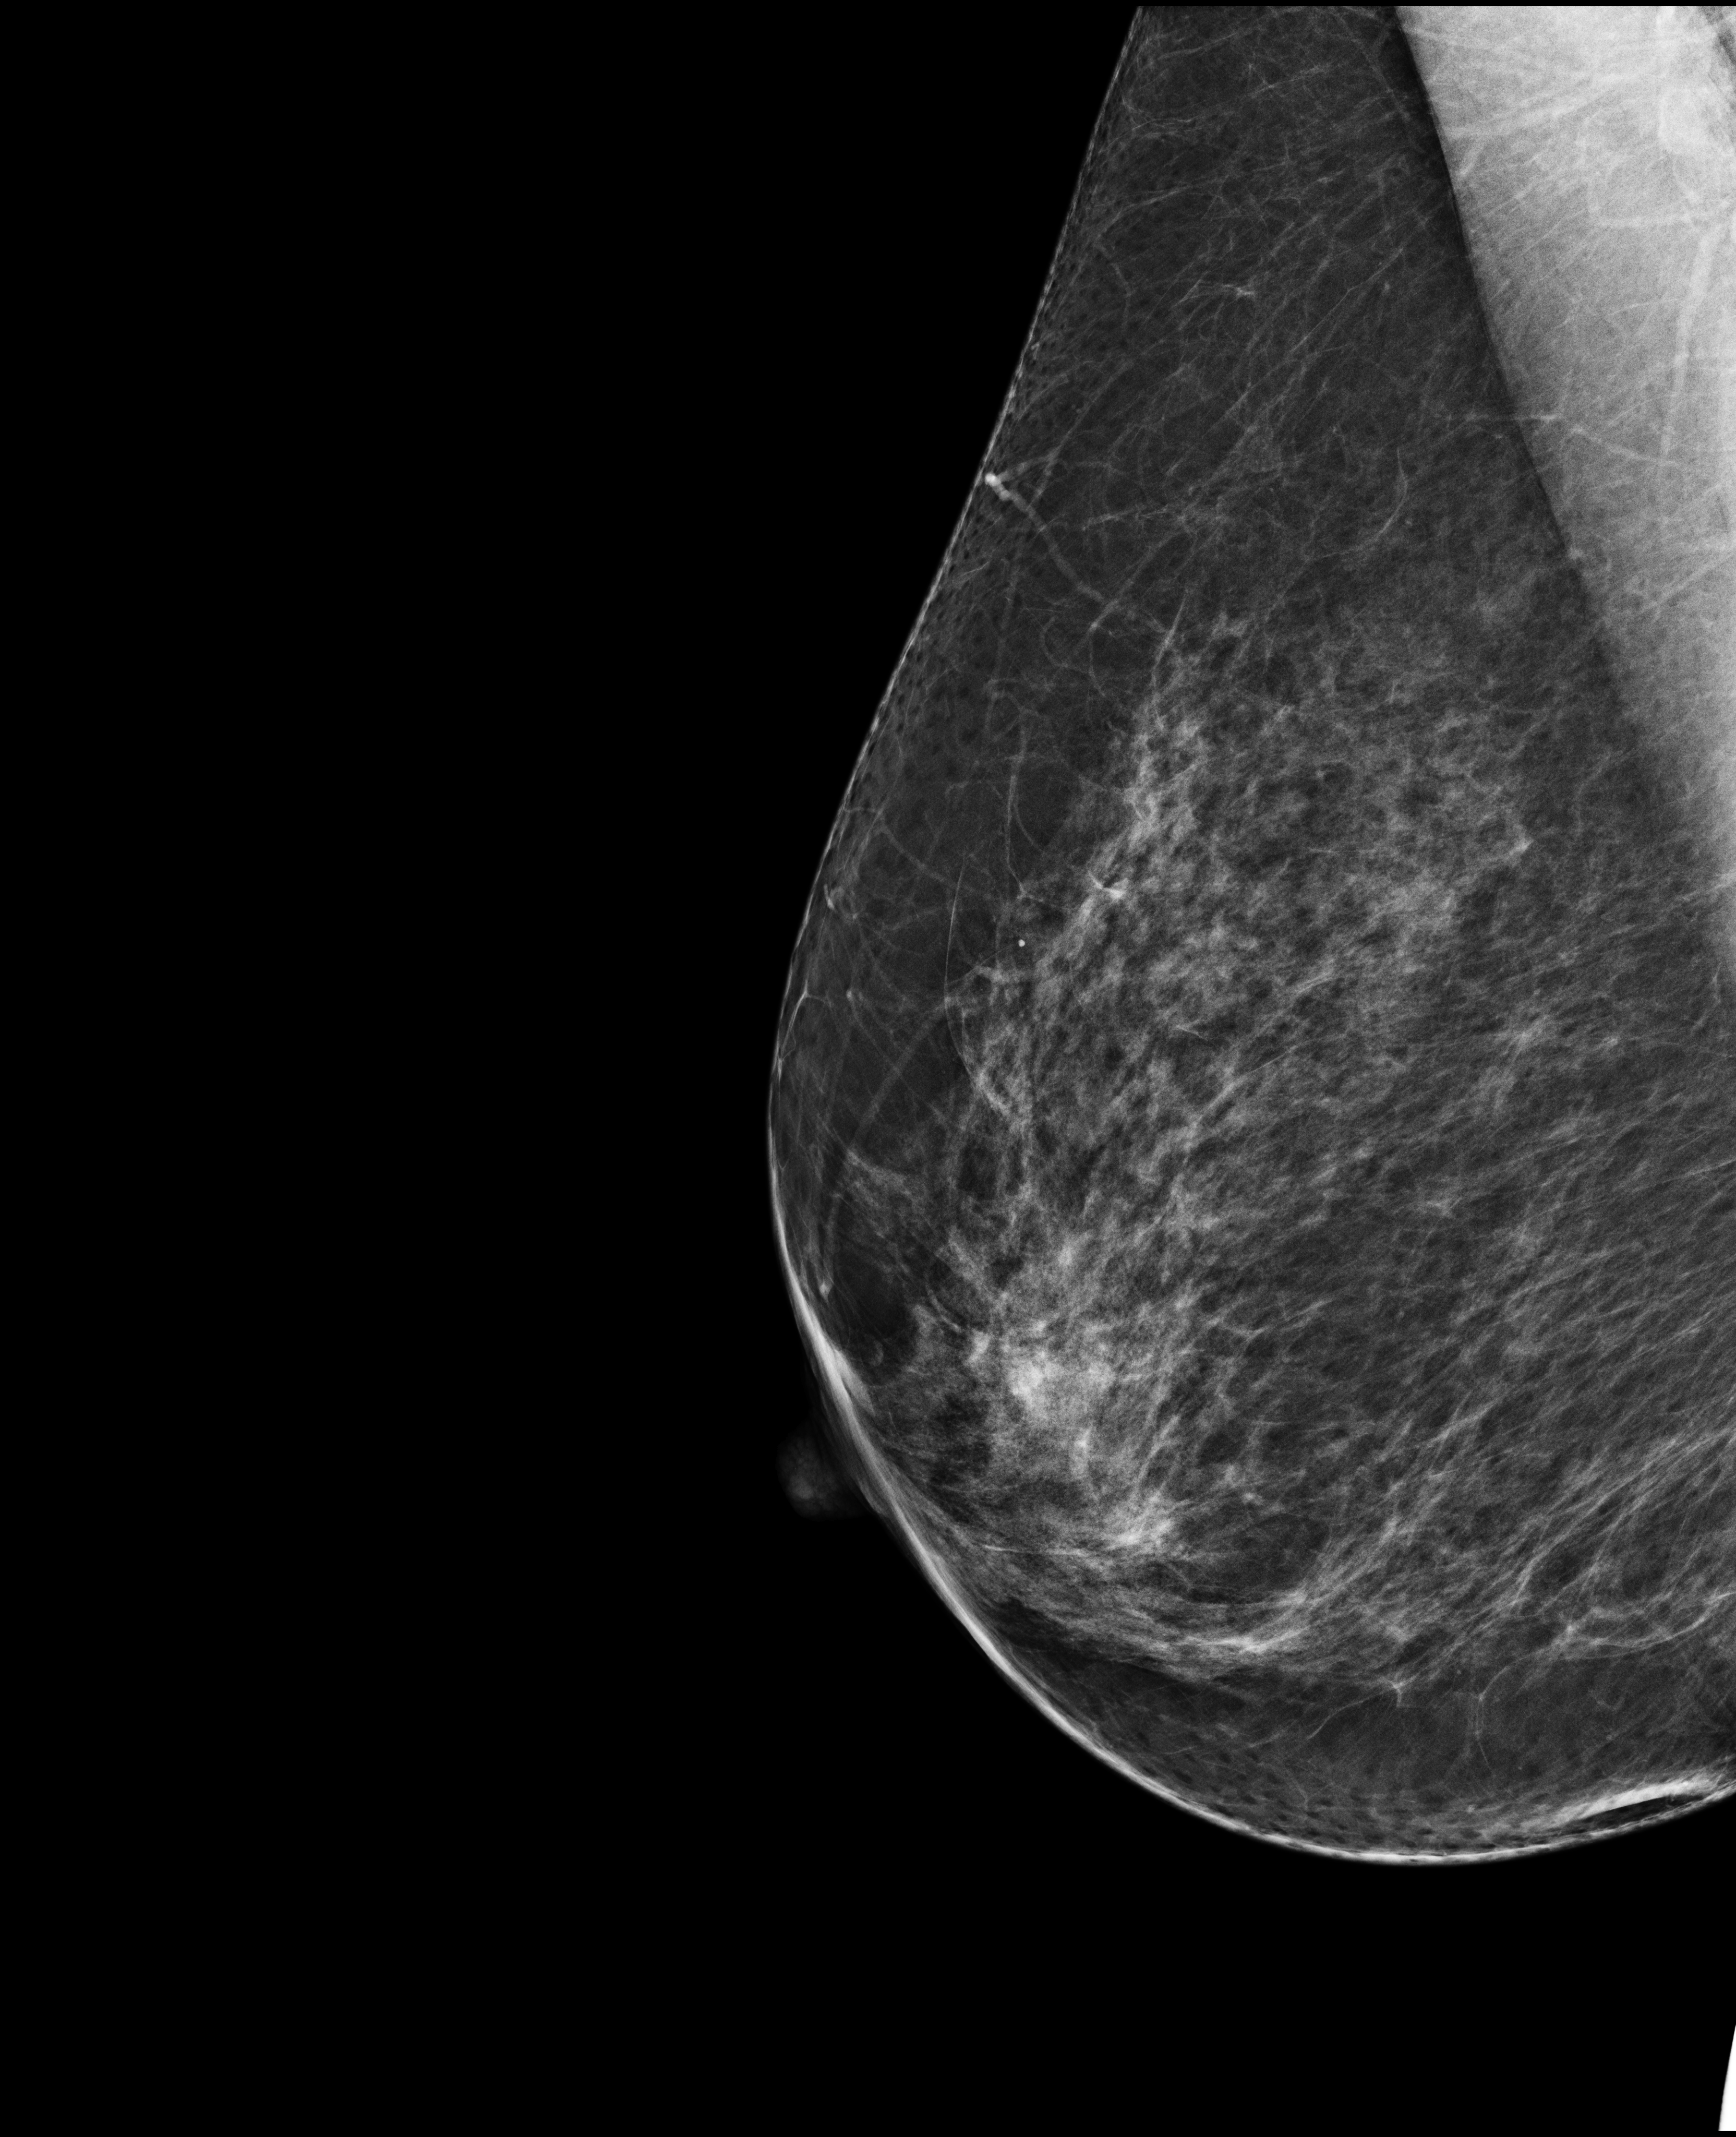
Full-field digital mammogram (FFDM), right breast, mediolateral (ML) view, diagnostic examination (additional views), compressed breast thickness 70 mm. Female patient, age 47 years.
- BI-RADS breast density category at the screening exam (both breasts, scale 1–4): 3
- final BI-RADS category for the screening round (tomosynthesis exam, both breasts): category 4
- recall: recalled for additional imaging after this screen